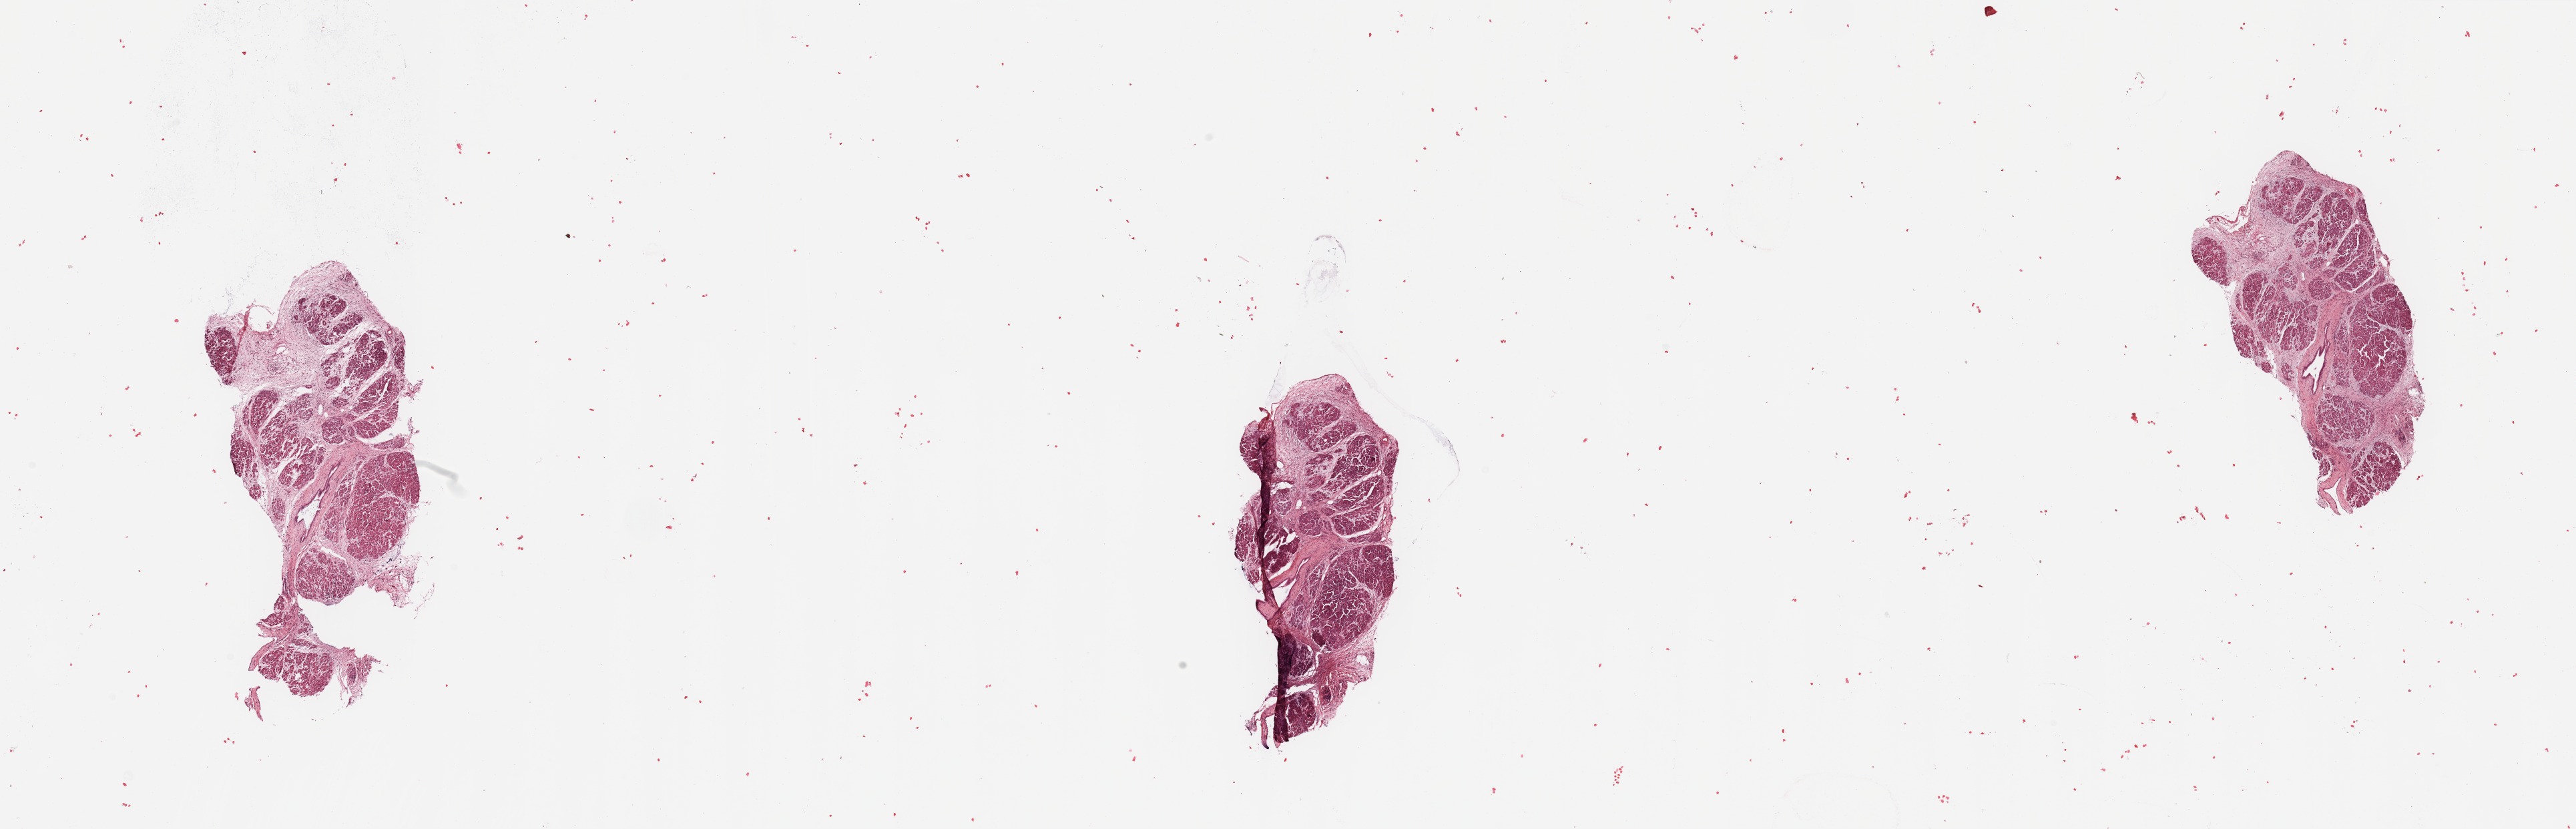
Digitized Hematoxylin and eosin (H&E) stained tissue section (whole slide) — a low-resolution overview of the entire scanned area, about 30.5 x 9.8 mm. Normal (non-tumour) tissue sample, sampled site: pancreas. 69-year-old female patient.
• this section: normal (non-tumour) tissue from the same patient
• patient diagnosis: Infiltrating duct carcinoma, NOS